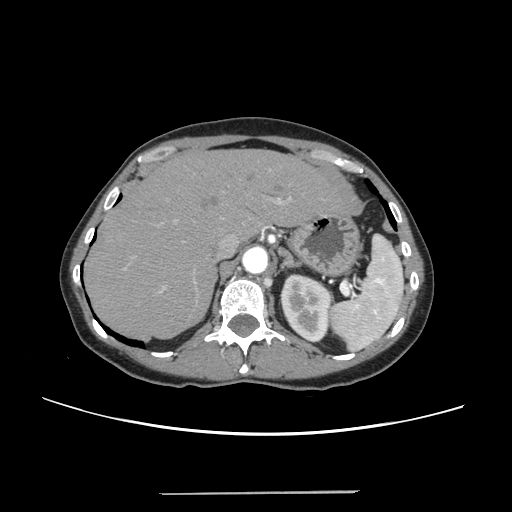
Contrast-enhanced abdominal CT, one axial slice; slice 180 of 240 in the series (ordered by position); intravenous contrast given; soft-tissue window (W 400 / L 40 HU); 512 × 512 image matrix, field of view 371 × 371 mm. Female patient, age 60 years. Case-level facts recorded for this patient, not image findings: diagnosis: colorectal cancer liver metastases, imaged before liver resection; multiple liver metastases: no; largest metastasis: 1.5 cm; chemotherapy before resection: yes.
Structures marked on this image (manually delineated by an expert):
- liver: bounding box [x1, y1, x2, y2] px = [87, 150, 348, 339]
- planned liver remnant (the part of the liver to remain after resection): [87, 150, 346, 339]
- portal vein (with intrahepatic branches): [133, 169, 291, 293]